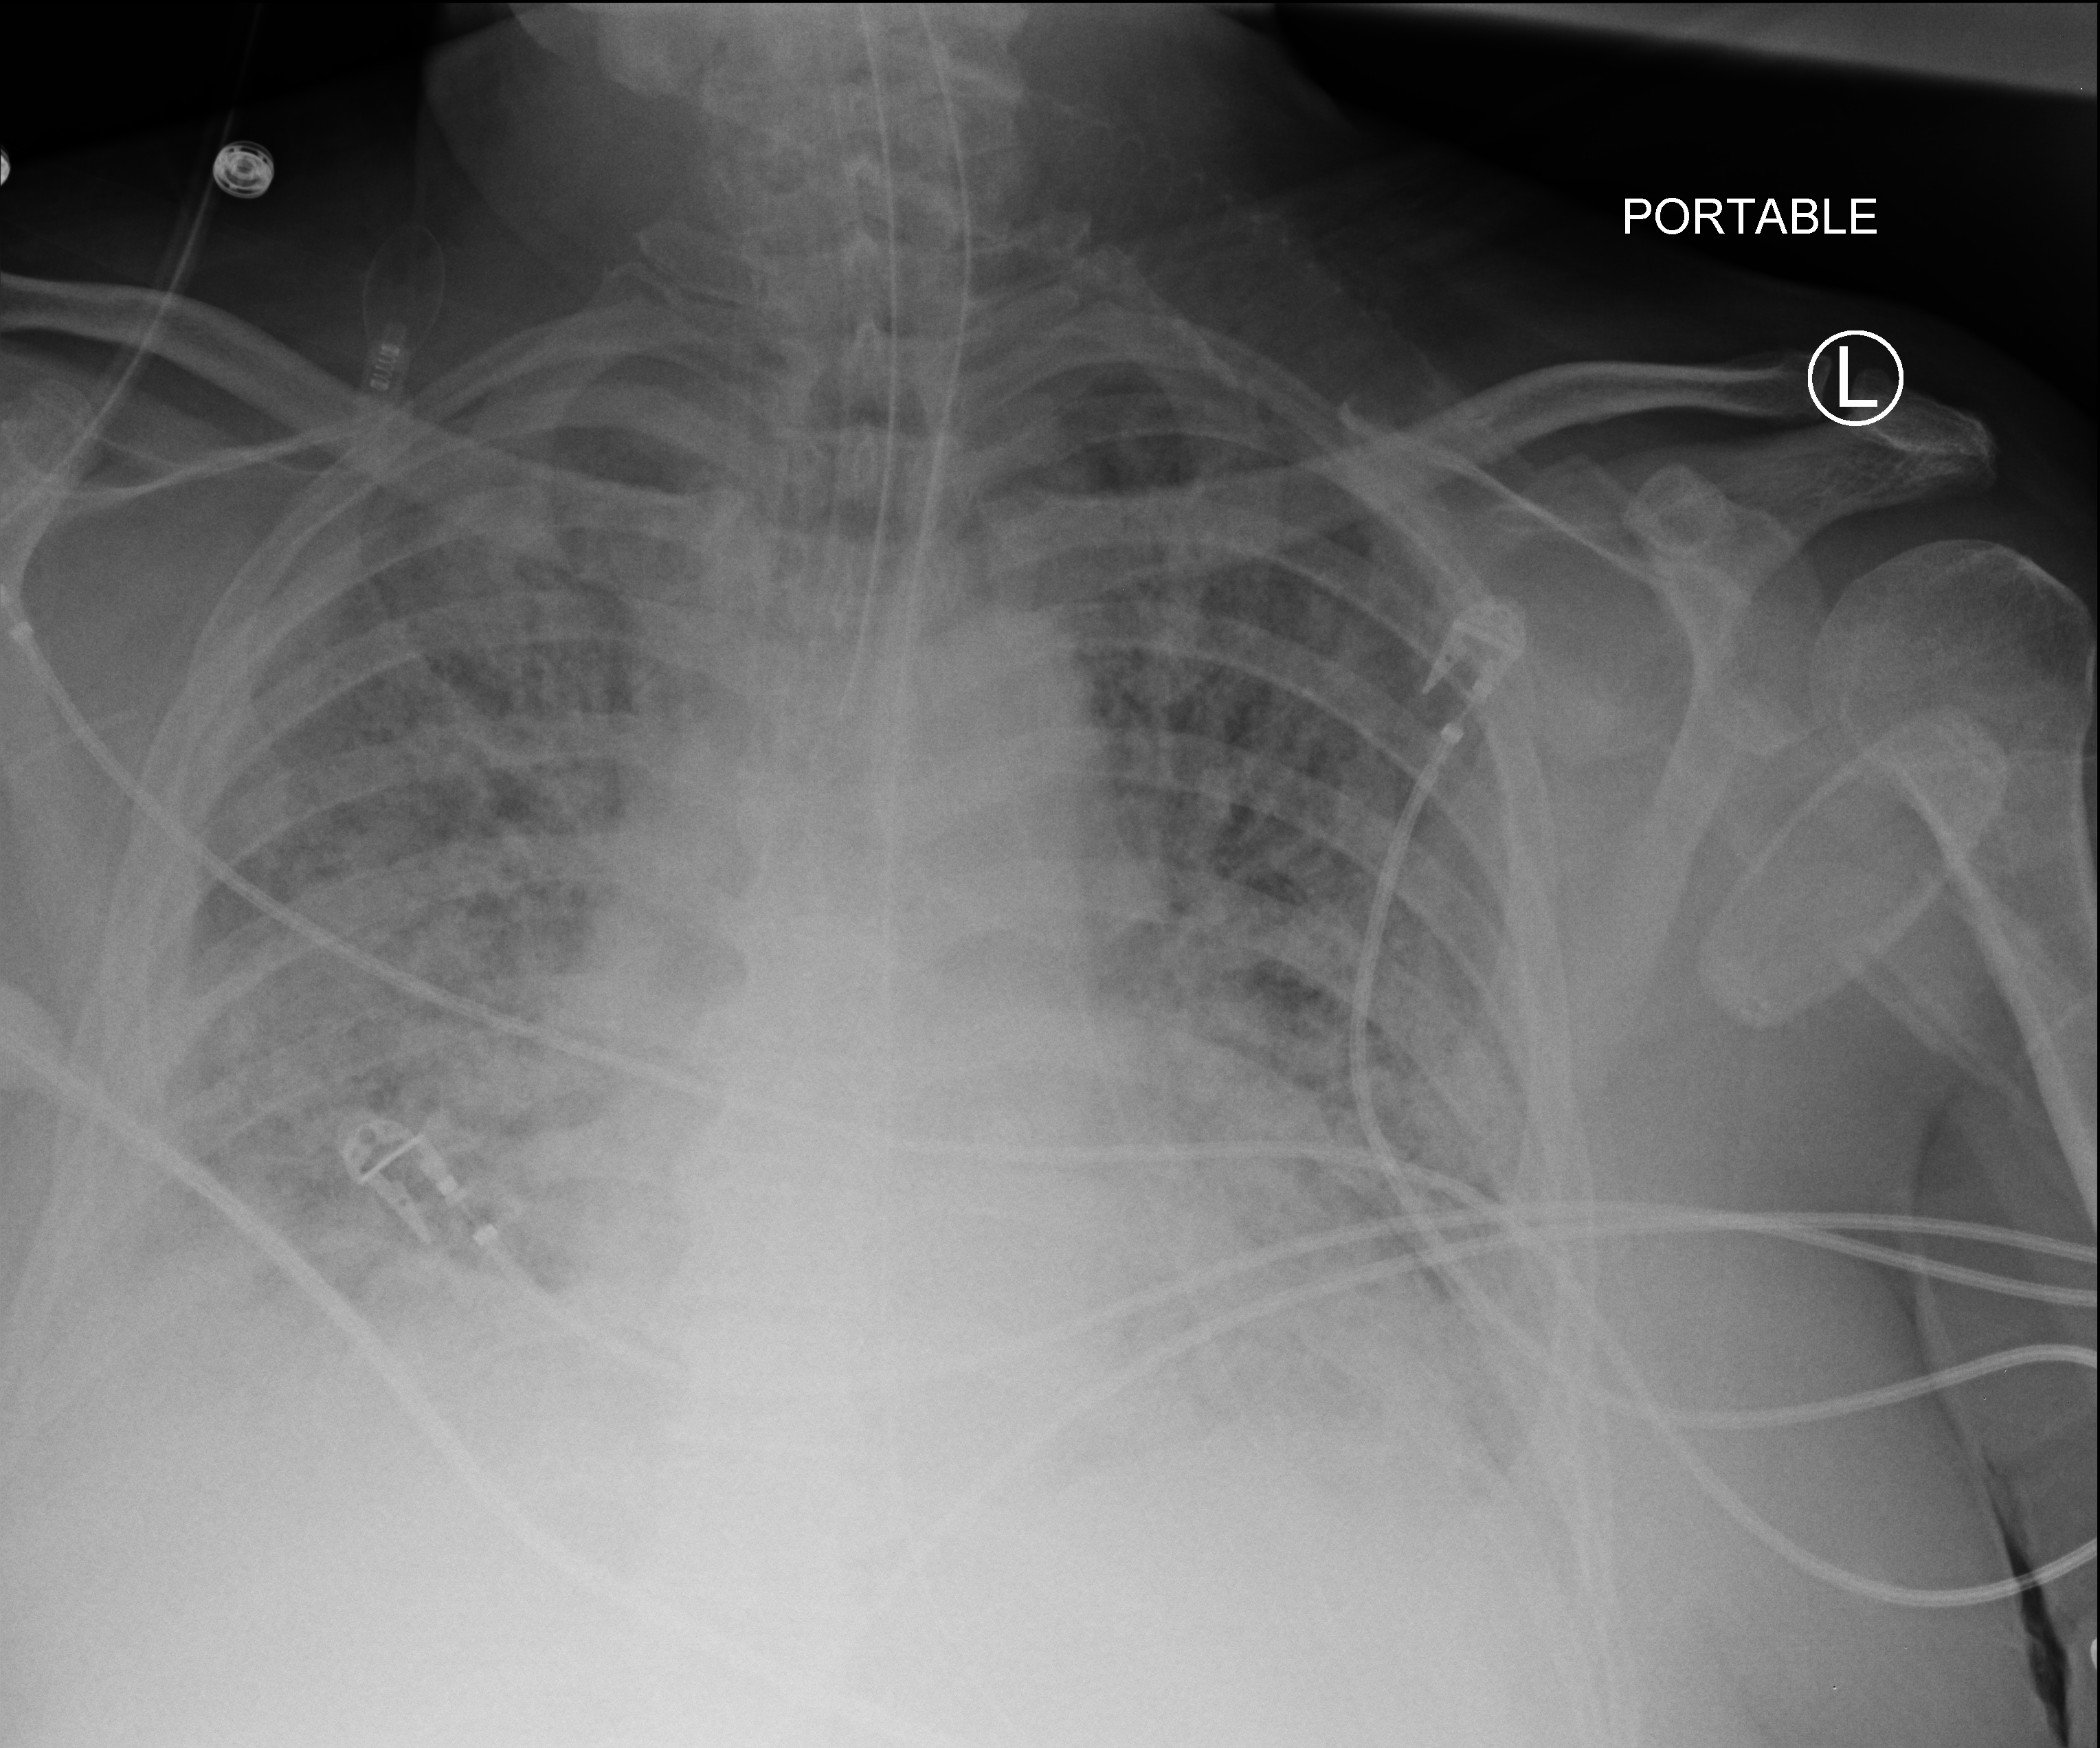
Chest X-ray (portable). Male patient hospitalised with COVID-19, age 60–74 years.
Admission-level facts for this patient (not findings on this image; timing relative to this image not recorded):
- hypertension (admission record): yes